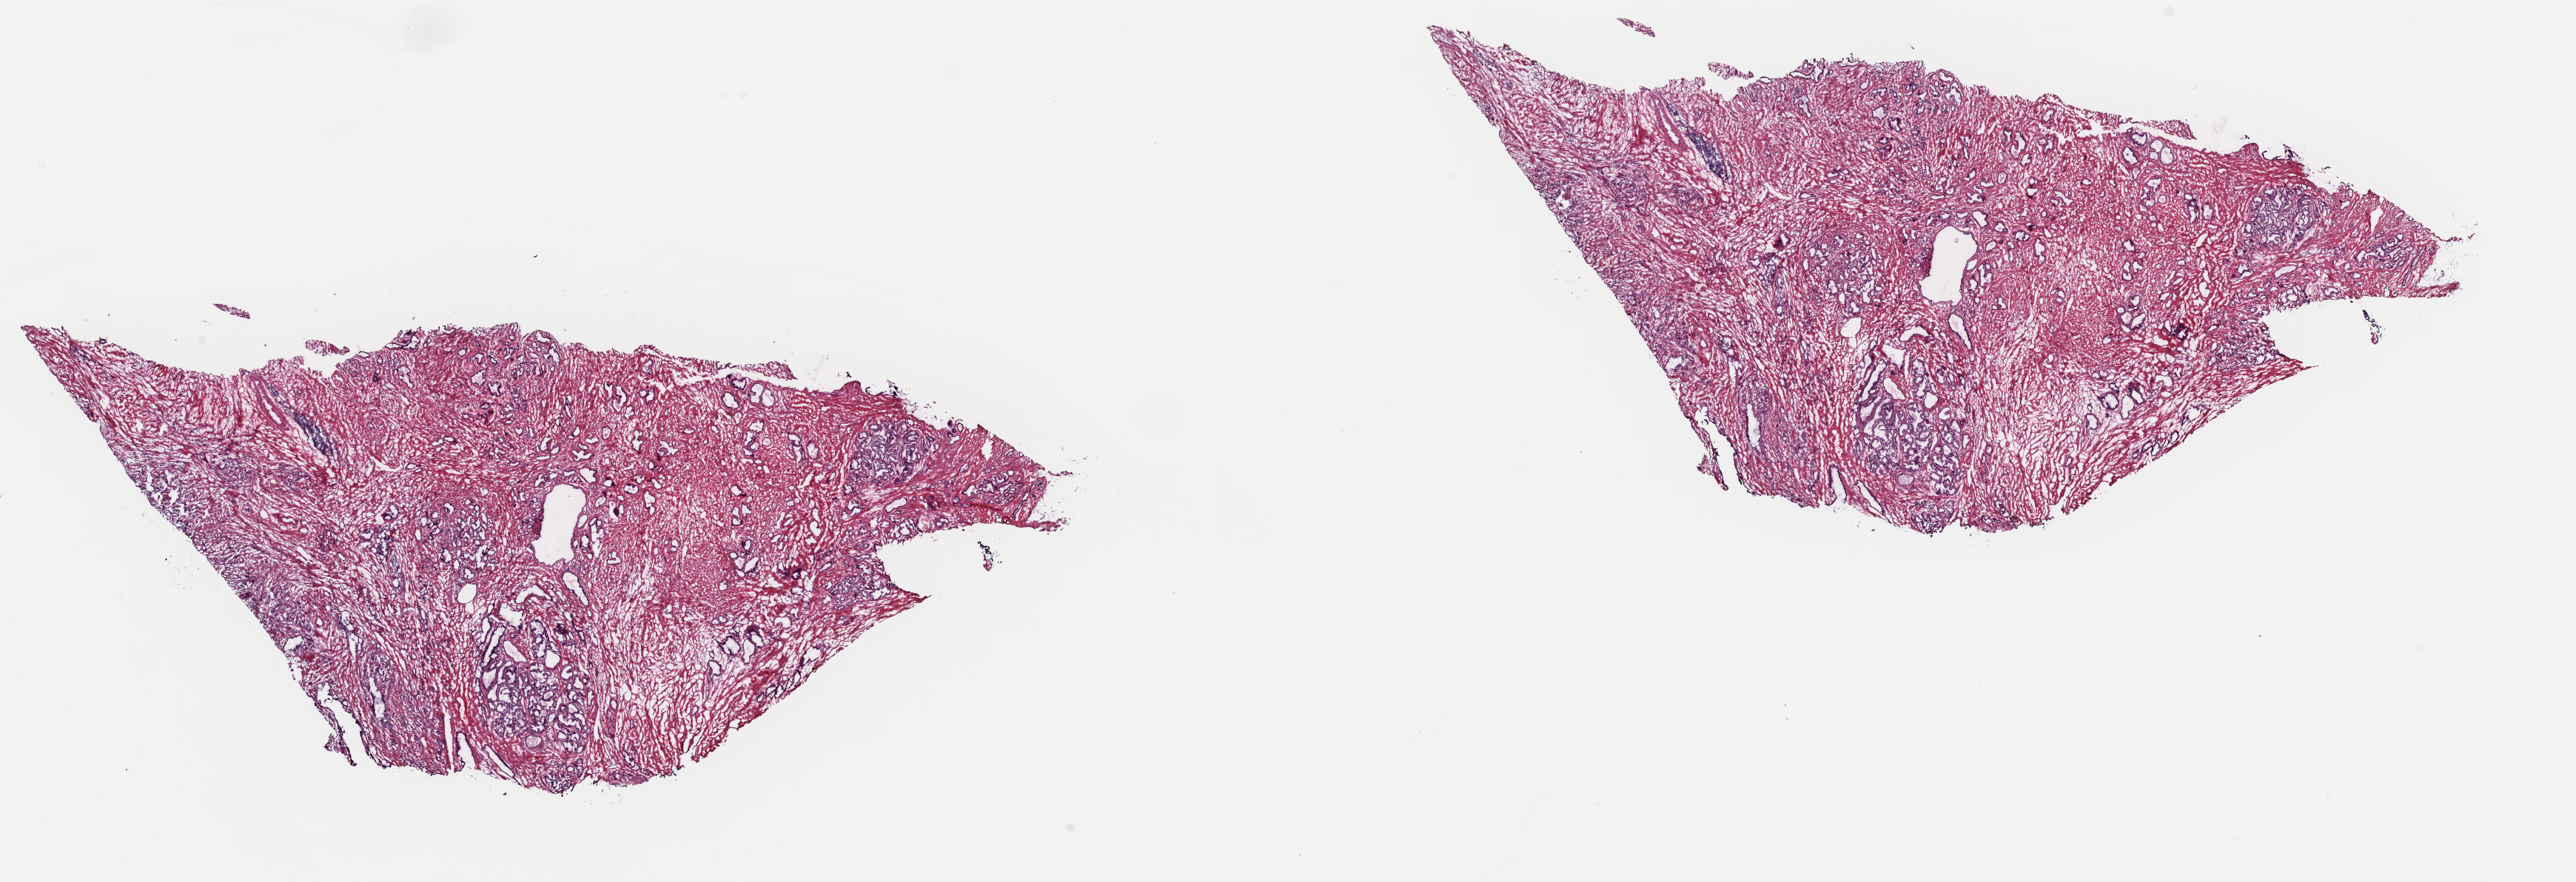
Whole-slide histology image, H&E, a low-resolution overview of the entire scanned area, about 27.5 x 9.4 mm (slide scanned at 40x), frozen section, primary tumour sample from the prostate. Male patient; age at initial diagnosis 77 years. Gleason score: 6 (3+3). Slide review estimates, as recorded: tumour cells 60%, tumour nuclei 60%, normal cells 10%, stromal cells 30%, necrosis 0%. Inflammatory infiltration, as recorded: lymphocyte infiltration 40%, monocyte infiltration 20%, neutrophil infiltration 20%.
• pathologic diagnosis: Adenocarcinoma, NOS (prostate gland)